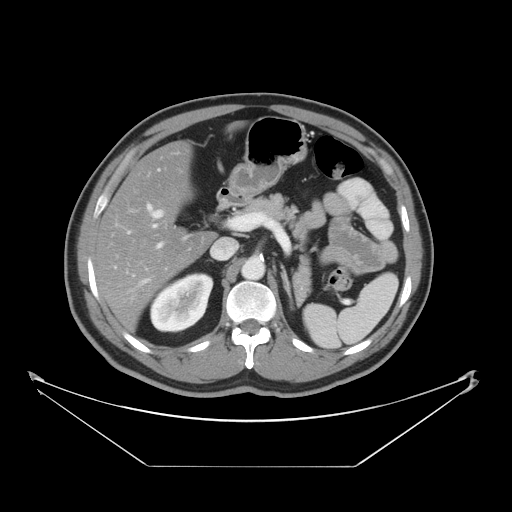
Contrast-enhanced abdominal CT, one axial slice; reconstruction kernel STANDARD; 120 kVp; intravenous contrast given; soft-tissue window (W 400 / L 40 HU); 5 mm slice thickness; 512 × 512 image matrix, field of view 465 × 465 mm. Male patient, age 57 years. Case-level facts recorded for this patient, not image findings: diagnosis: colorectal cancer liver metastases, imaged before liver resection; multiple liver metastases: no; largest metastasis: 3.3 cm; chemotherapy before resection: yes.
Outlined on this slice (expert manual segmentation):
- hepatic veins: box from (x=149, y=209) to (x=164, y=220) px
- liver: (x=98, y=143)–(x=214, y=330)
- planned liver remnant (the part of the liver to remain after resection): (x=98, y=143)–(x=214, y=331)
- portal vein (with intrahepatic branches): (x=149, y=206)–(x=249, y=247)